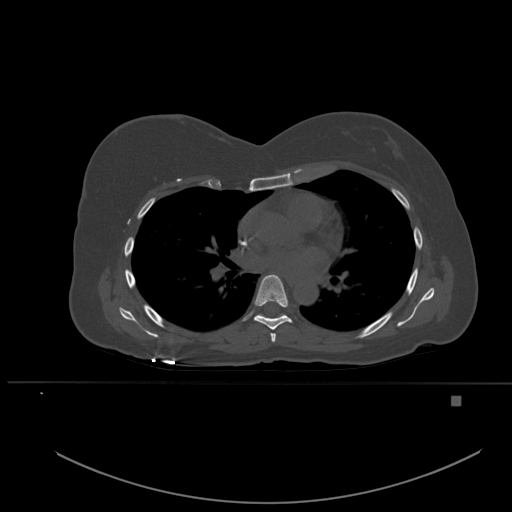
CT including the spine, one axial slice; position 349 of 651 along the scan axis; bone window (W 1800 / L 400 HU); 1.5 mm slice thickness; 512 × 512 image matrix, field of view 443 × 443 mm. Patient: female, 49 years. Case-level facts recorded for this patient, not image findings: primary cancer: breast; vertebrae with lytic lesions (as recorded): L3, T12, L4.
Structures marked on this image (semi-automatically segmented with operator editing):
- T5 vertebra: bounding box (x1, y1, x2, y2) in pixels: (270, 333, 276, 342)
- T6 vertebra: (254, 274, 292, 330)